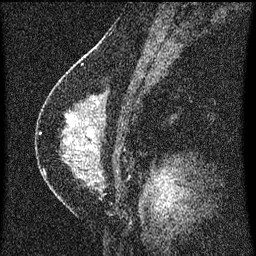
Breast MRI (dynamic contrast-enhanced), one sagittal slice. Slice 36 of 60 in the series (ordered by position). Dynamic contrast-enhanced series, image 2 of 3 at this slice position (ordered by acquisition). 1.5 T. TE 4.2 ms, TR 8 ms. 2 mm slice thickness. 256 × 256 image matrix. Female patient, age 47 years.
Outlined on this slice (semi-automatically segmented with operator editing):
- analysis volume of interest (the breast-tissue region the enhancement analysis was run in; not a lesion): box from (x=42, y=92) to (x=132, y=199) px
- tumour enhancement mask (voxels above the 70 % enhancement threshold inside the analysis volume of interest): (x=69, y=124)–(x=94, y=149)